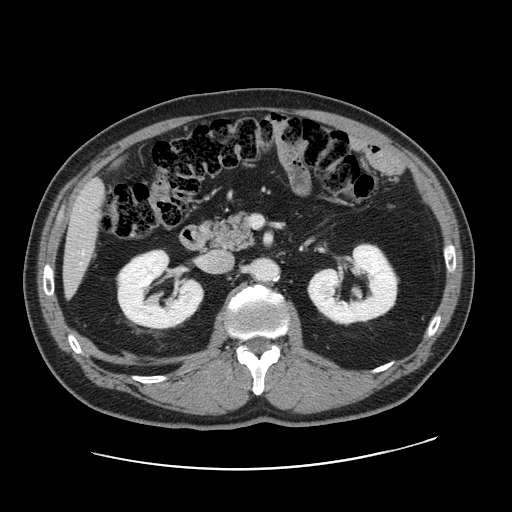
Contrast-enhanced abdominal CT, one axial slice. Slice 75 of 178 in the series (ordered by position). Soft-tissue window (W 400 / L 40 HU). 2.5 mm slice thickness. 512 × 512 image matrix, field of view 403 × 403 mm. Male patient, age 63 years. From the clinical record (not read from this slice): diagnosis: colorectal cancer liver metastases, imaged before liver resection; multiple liver metastases: yes; largest metastasis: 8 cm.
Outlined on this slice (manually delineated by an expert):
- liver: bounding box [x1, y1, x2, y2] px = [64, 180, 104, 292]